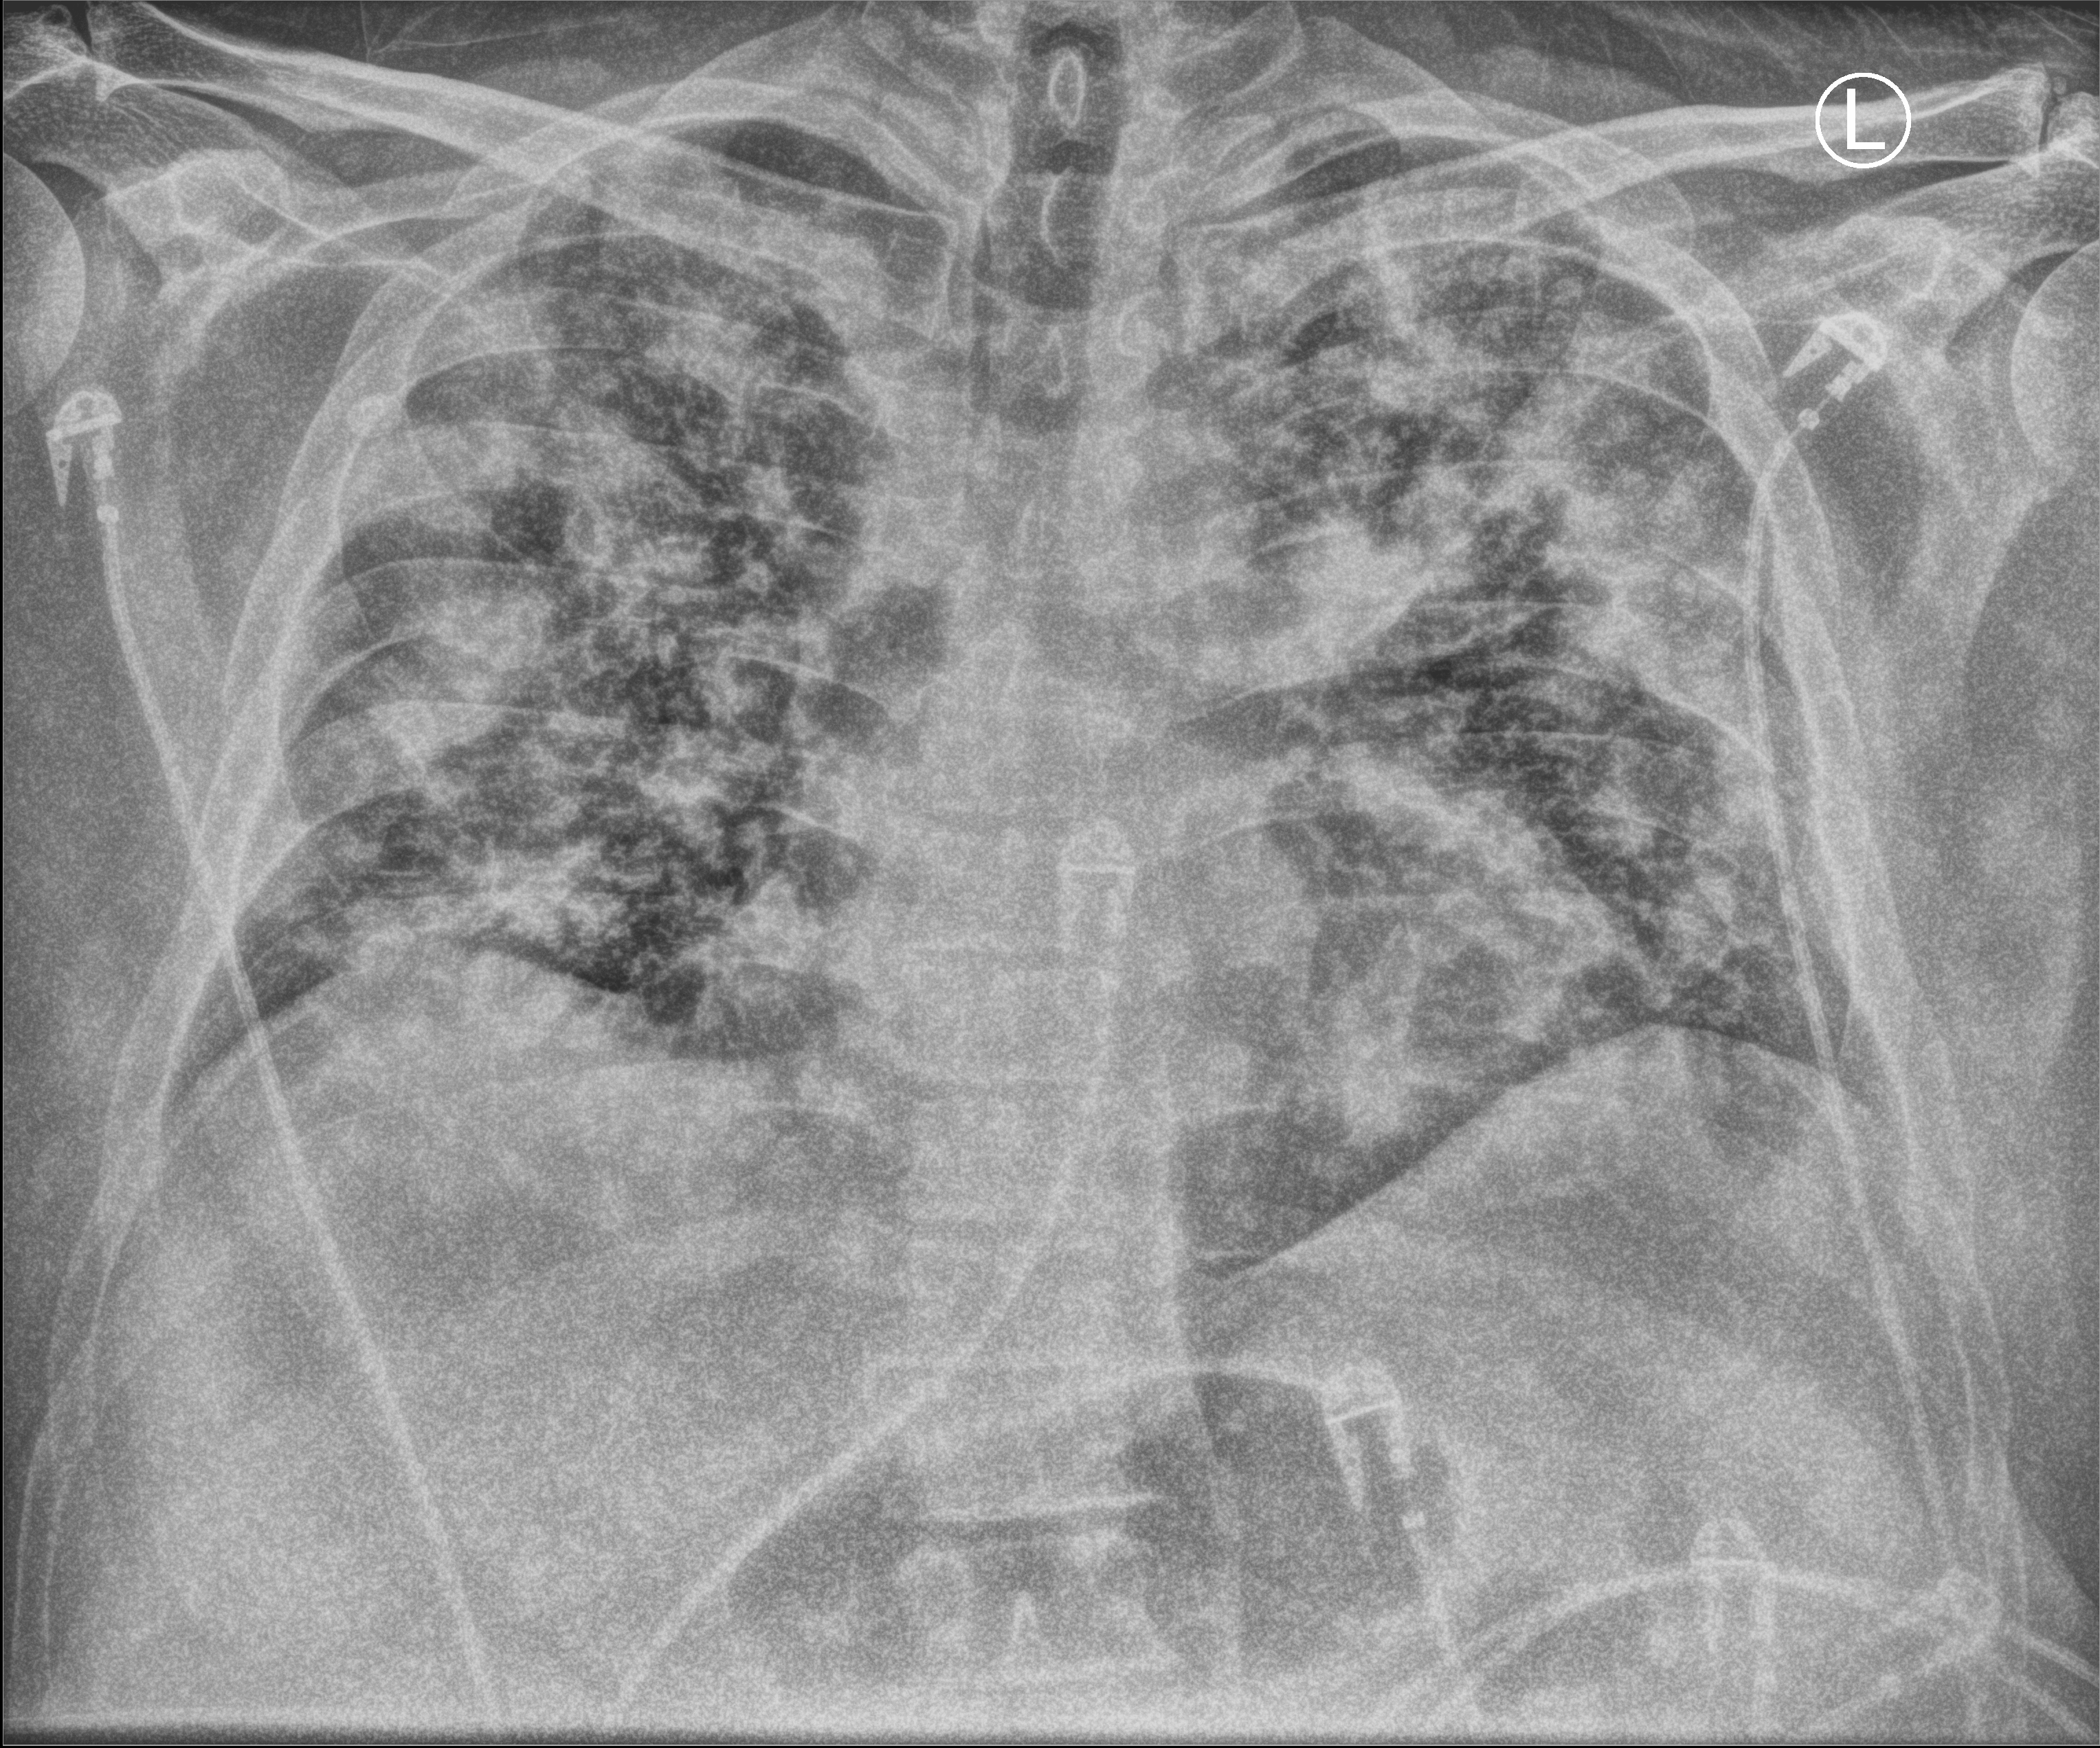
Bedside chest radiograph (computed radiography); anteroposterior (AP) projection. Male patient hospitalised with COVID-19, age 18–59 years.
Admission-level facts for this patient (not findings on this image; timing relative to this image not recorded):
- length of hospital stay: 20 days
- other chronic lung disease (admission record): yes
- admitted to intensive care during this hospital stay: yes